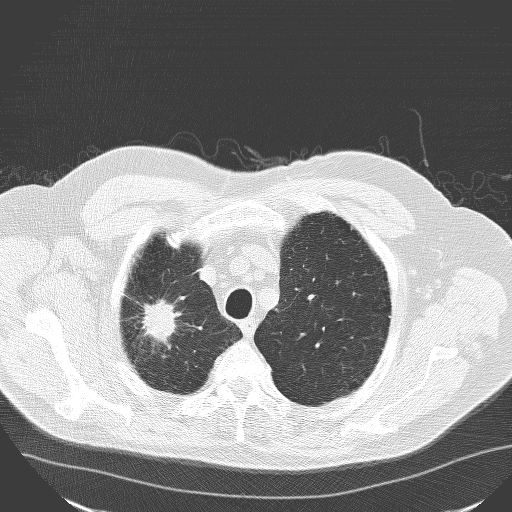
Low-dose screening chest CT, one axial slice; position 136 of 160 along the scan axis; 120 kVp; lung window (W 1500 / L -600 HU); 512 × 512 image matrix, field of view 400 × 400 mm.
Structures marked on this image (expert manual segmentation):
- lesion 1 (tumor, upper lobe of right lung): bounding box <142,300,179,343> (left, top, right, bottom; pixels)